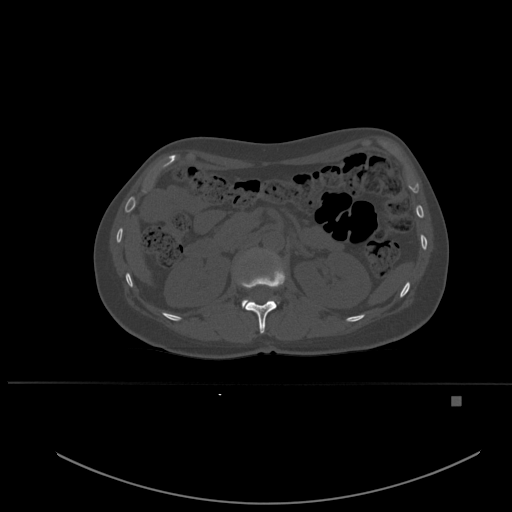
CT including the spine, one axial slice. Bone window (W 1800 / L 400 HU). 512 × 512 image matrix, field of view 443 × 443 mm. Patient: female, 49 years. Case-level facts recorded for this patient, not image findings: primary cancer: breast; vertebrae with lytic lesions (as recorded): L3, T12, L4.
Outlined on this slice (semi-automatically segmented with operator editing):
- L1 vertebra: bounding box (x1, y1, x2, y2) in pixels: (242, 299, 279, 308)
- T12 vertebra: (240, 261, 286, 334)